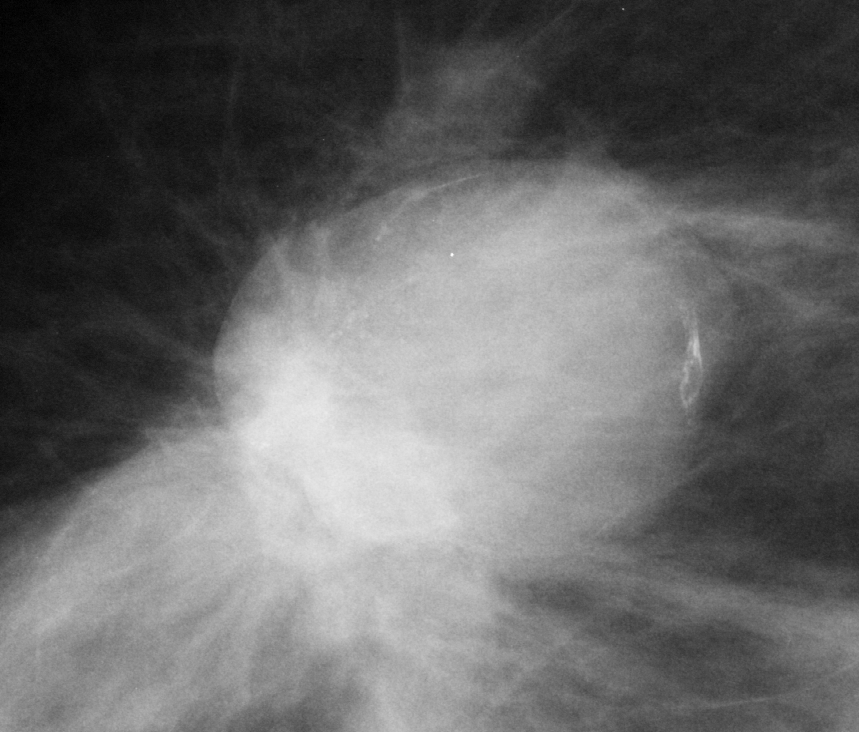
Crop from a digitized film mammogram around one marked abnormality; right breast; MLO view.
Finding: mass, shape lobulated, margins spiculated; BI-RADS assessment category 5; subtlety rating 5 on a 1 (subtle) to 5 (obvious) scale; pathology (as recorded): malignant.